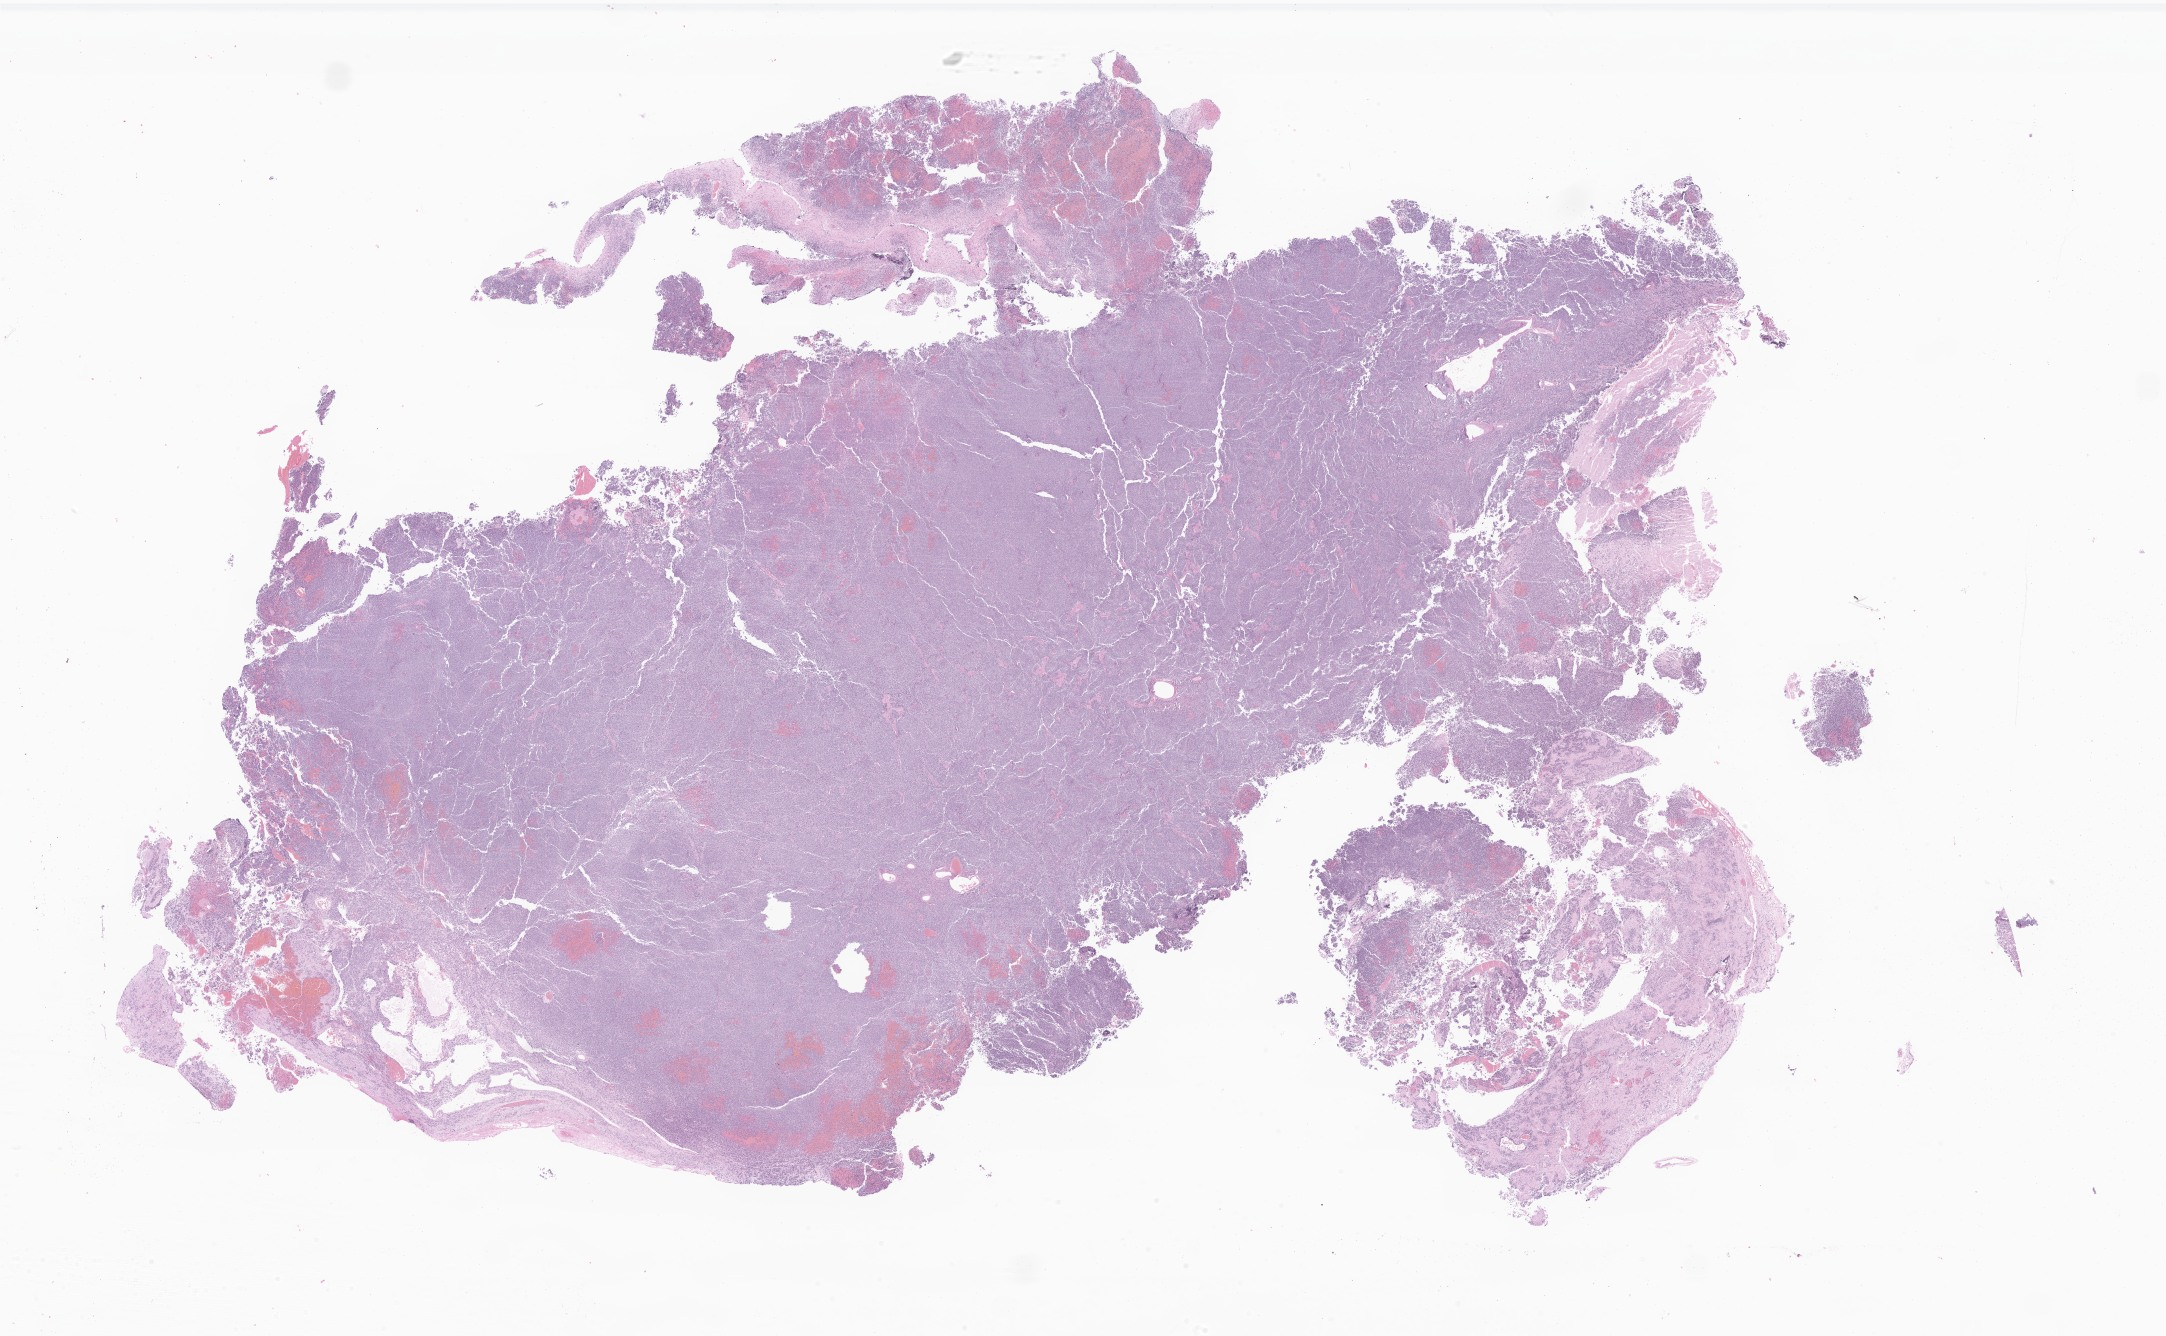
Hematoxylin and eosin (H&E) whole-slide image of tumor tissue from the brain — whole scanned area (about 36.5 x 22.5 mm) shown as a low-resolution overview. Formalin-fixed paraffin-embedded section. Male patient, age 107 months (8 years 11 months).
- recorded diagnosis: Medulloblastoma, NOS